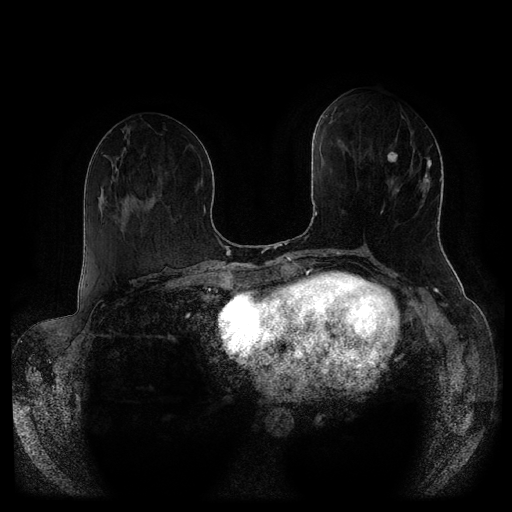
Breast MRI (dynamic contrast-enhanced, multi-phase), one axial slice; position 41 of 116 along the scan axis; dynamic contrast-enhanced series, time point 2 of 5 at this slice position (early post-contrast); 1.5 T; TE 2.6 ms, TR 5.3 ms; 512 × 512 image matrix, field of view 370 × 370 mm. Patient: female, 51 years.
Outlined on this slice (semi-automatically segmented with operator editing):
- breast lesion (labelled 'tumour' in the annotation; benign lesions carry a separate 'benign' label): bounding box (x1, y1, x2, y2) in pixels: (387, 152, 398, 163)